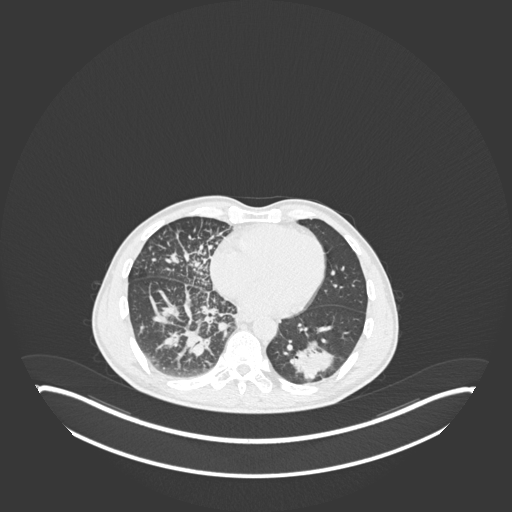
Chest CT, one axial slice. Position 82 of 237 along the scan axis. Reconstruction kernel B30f. 120 kVp. Lung window (W 1500 / L -600 HU). 1 mm slice thickness. 512 × 512 image matrix, field of view 500 × 500 mm. Patient: male, 49 years. From the clinical record (not read from this slice): clinical TNM (as recorded): T2b N1 M0.
Annotated regions visible in this slice (bounding box drawn by a radiologist):
- lung tumour (recorded histology: adenocarcinoma): bounding box [x1, y1, x2, y2] px = [284, 339, 343, 383]